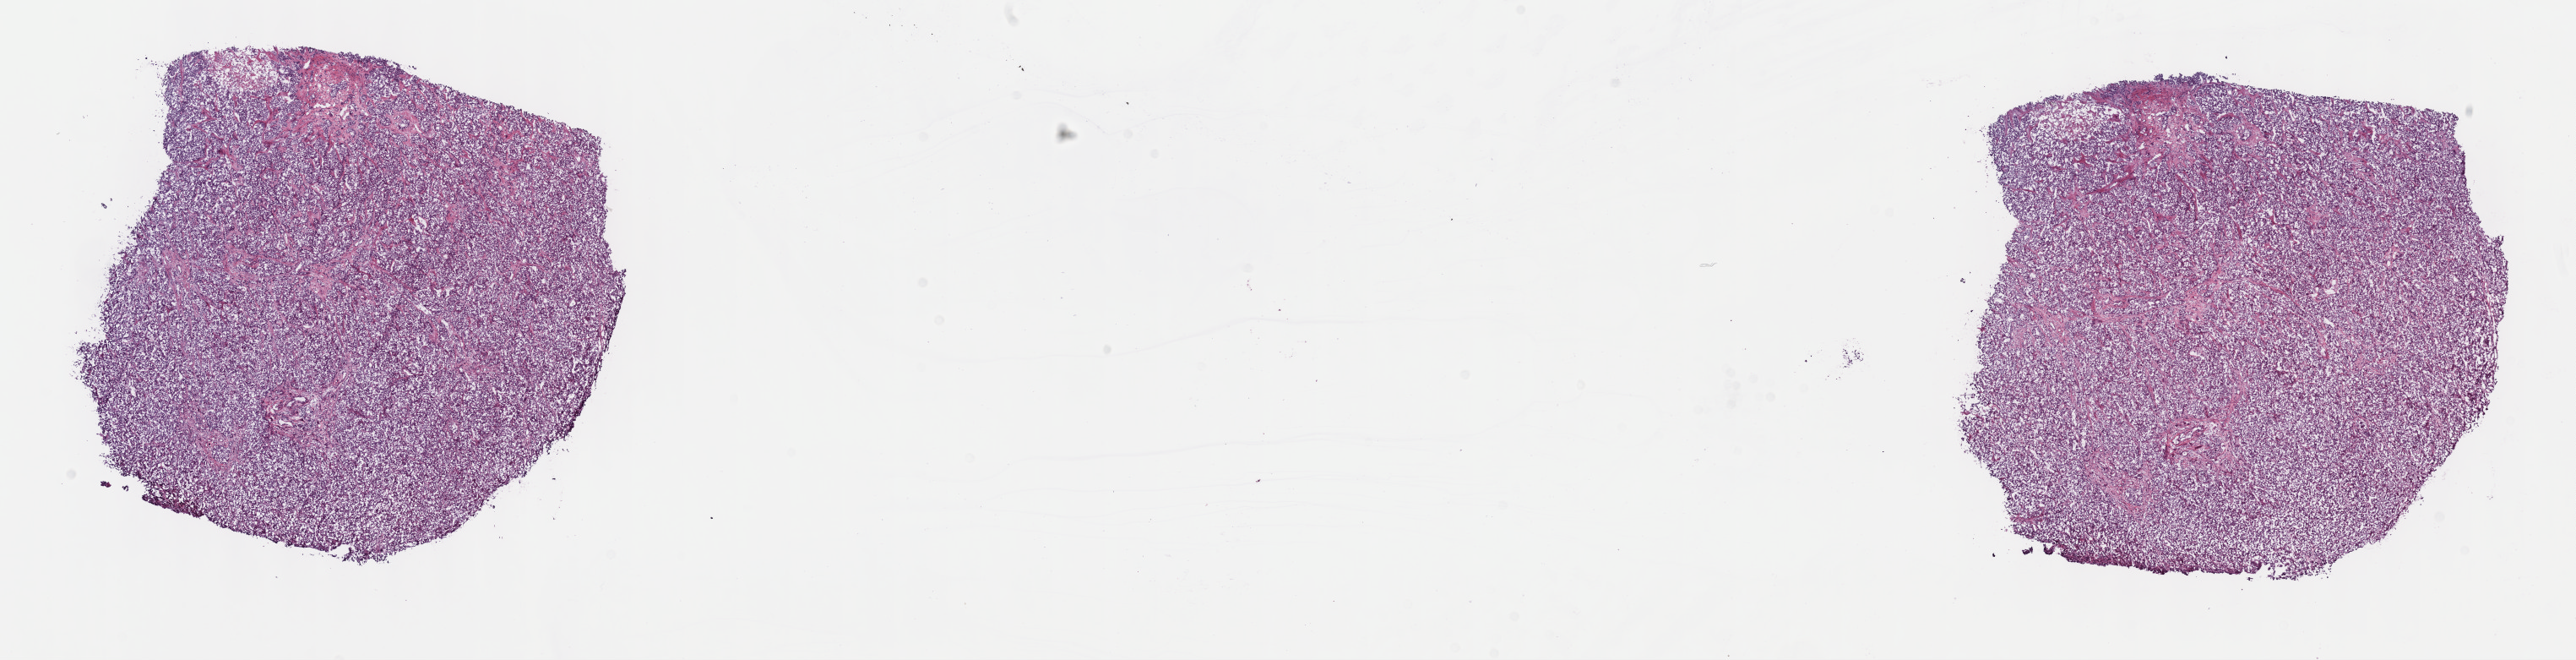
Whole-slide histology image, H&E-stained, whole scanned area (about 24.7 x 6.3 mm, slide scanned at 40x) shown as a low-resolution overview, frozen section from the top of the tissue portion, sample: primary tumour, bile duct. Patient: male, age at initial diagnosis 57 years. Histologic grade: G3 (poorly differentiated). Slide review estimates, as recorded: tumour cells 85%, tumour nuclei 85%, normal cells 0%, stromal cells 15%, necrosis 0%. Infiltration values recorded for this section: lymphocyte infiltration 2%, monocyte infiltration 1%, neutrophil infiltration 3%.
AJCC pathologic stage: I. TNM: T1 N0 M0. Diagnosis: Cholangiocarcinoma (intrahepatic bile duct).